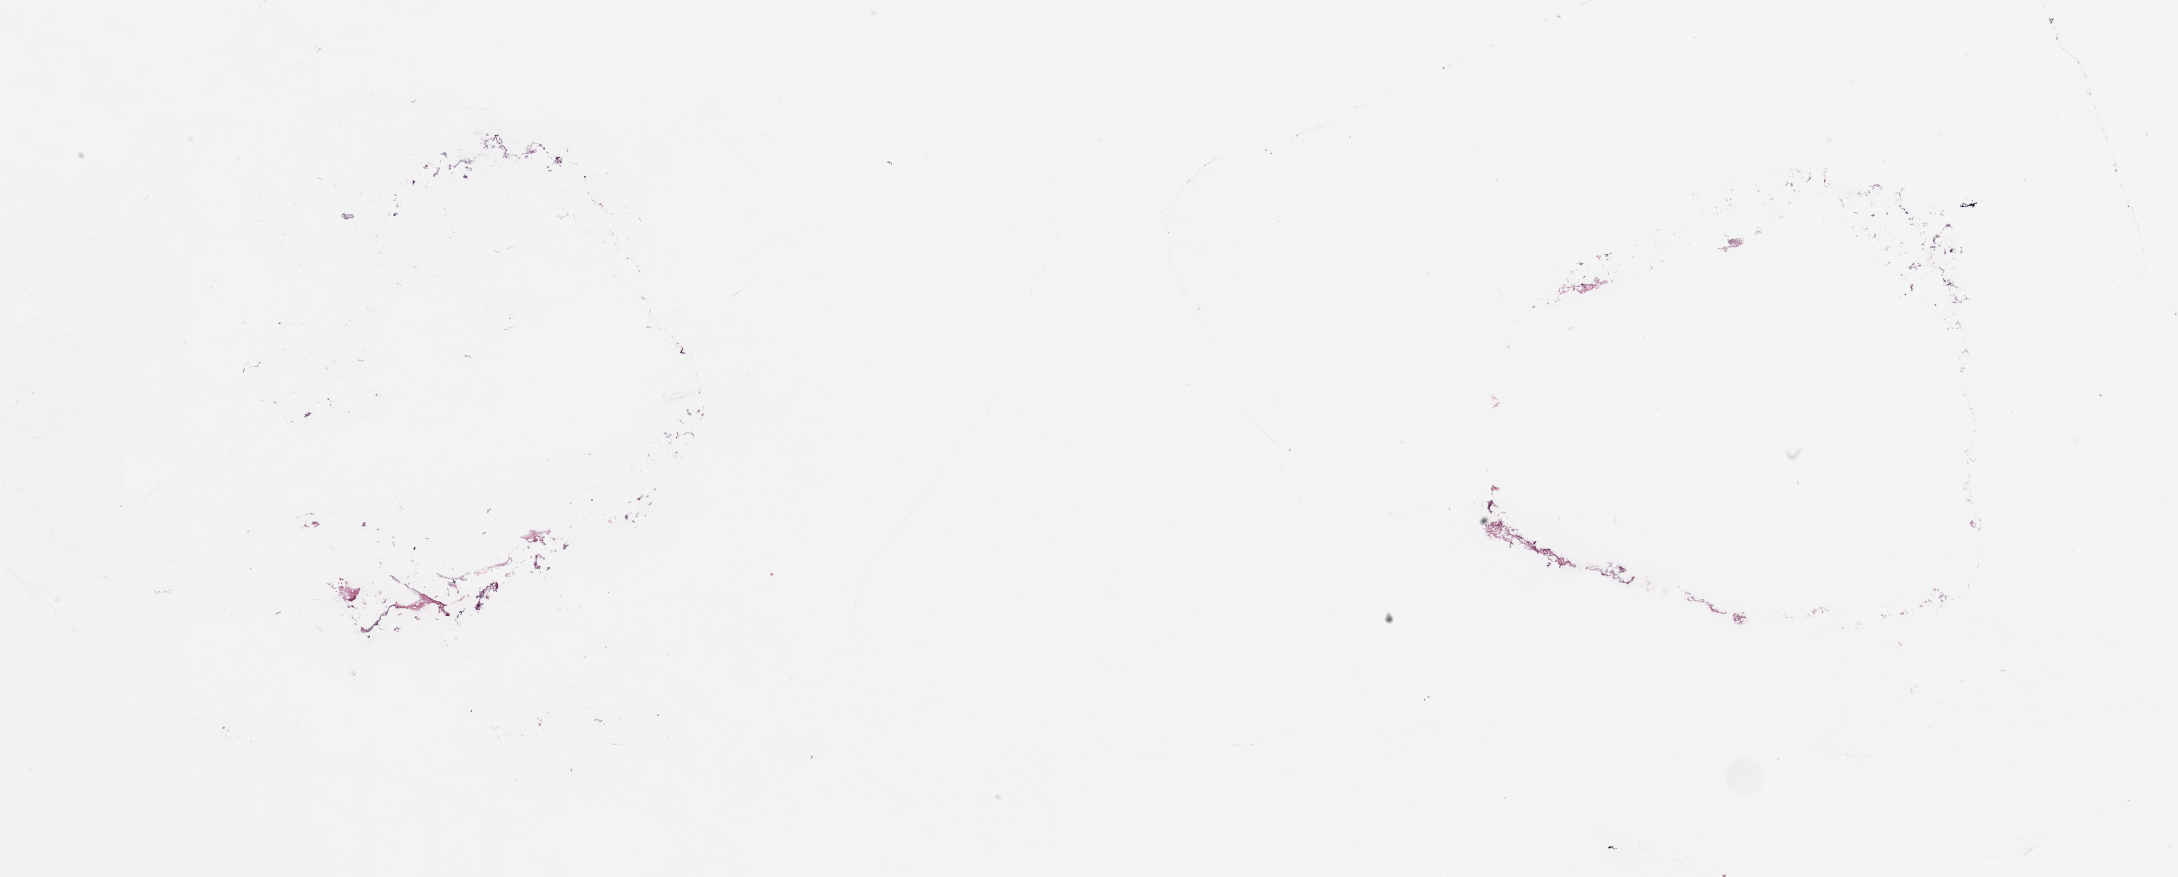
Digitized H&E tissue section (whole slide) — low-resolution overview of the scanned area, about 34.5 x 13.9 mm. Breast, tissue type not recorded.
Patient diagnosis (cohort enrolment): breast cancer (breast).